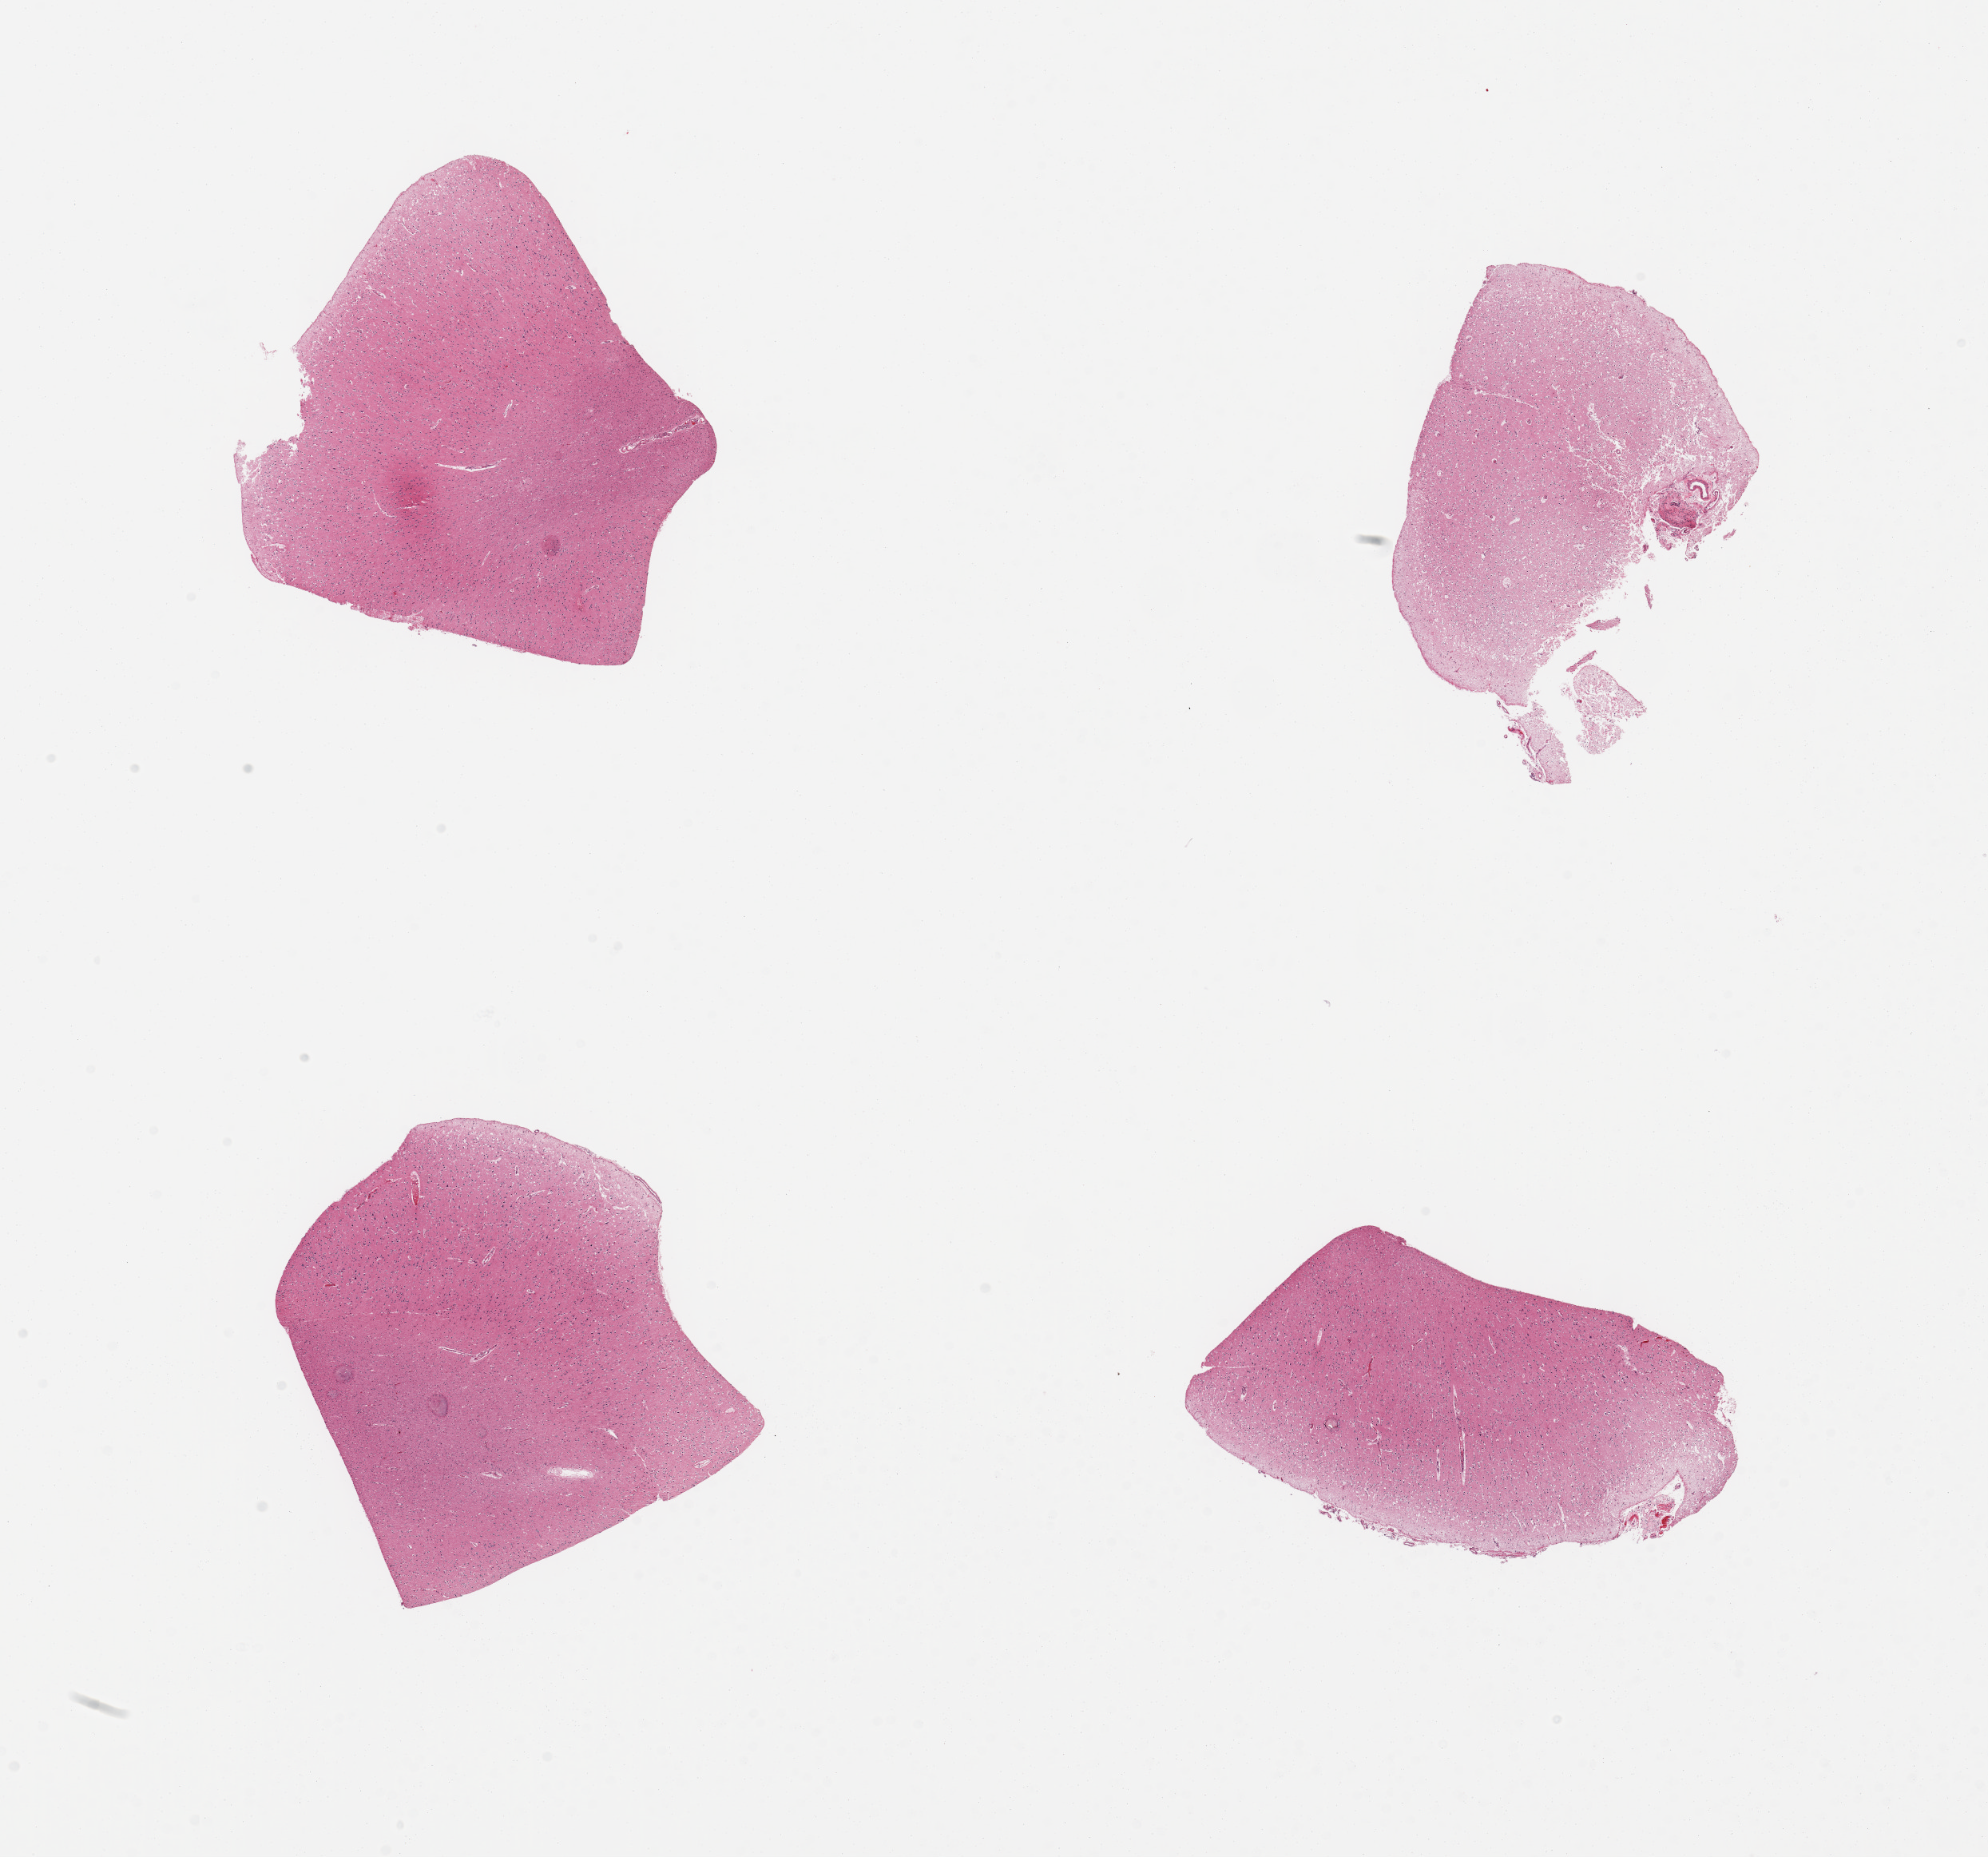
H&E whole-slide image — low-resolution overview of the scanned area, about 19.7 x 18.4 mm; PAXgene-fixed paraffin-embedded (PFPE) section; section of cerebral cortex (target tissue); tissue donor sample. Donor: male.
Pathologist's review note for this sample: 4 pieces, cerebral cortex, no abnormalities.